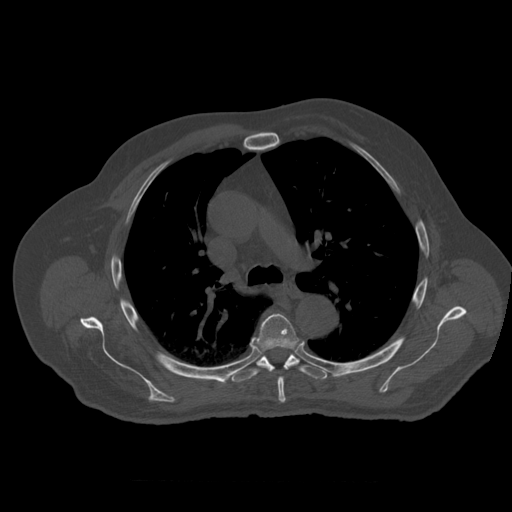
CT including the spine, one axial slice; bone window (W 1800 / L 400 HU); 1.25 mm slice thickness; 512 × 512 image matrix, field of view 407 × 407 mm. Patient age 73 years. From the clinical record (not read from this slice): primary cancer: prostate; vertebrae with lytic lesions (as recorded): L2.
Structures marked on this image (semi-automatic segmentation, software-assisted and operator-edited):
- T5 vertebra: bounding box <256,314,303,403> (left, top, right, bottom; pixels)
- T6 vertebra: <231,354,327,383>